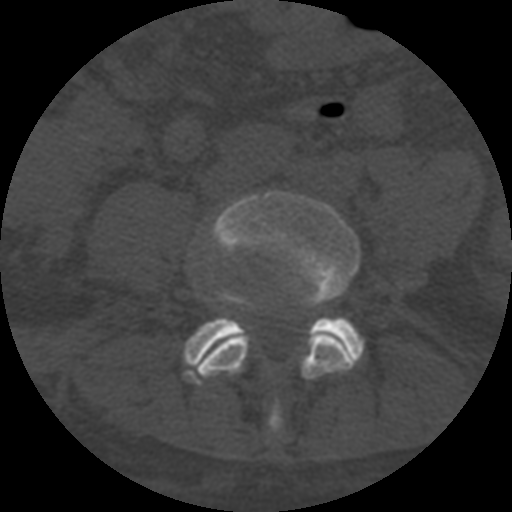
CT including the spine, one axial slice. Slice 198 of 708 in the series (ordered by position). One of 3 acquisitions stored at this slice position. Bone window (W 1800 / L 400 HU). 512 × 512 image matrix, field of view 160 × 160 mm. Patient age 55 years. Case-level facts recorded for this patient, not image findings: primary cancer: colon; vertebrae with lytic lesions (as recorded): T12, L1, L5.
Structures marked on this image (semi-automatically segmented with operator editing):
- L4 vertebra: box from (x=198, y=190) to (x=360, y=432) px
- L5 vertebra: (x=183, y=293)–(x=364, y=384)